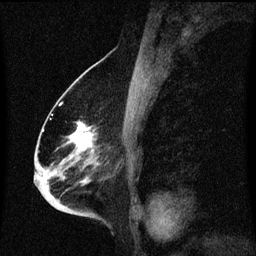
Breast MRI (dynamic contrast-enhanced), one sagittal slice. Slice 37 of 60 in the series (ordered by position). Dynamic contrast-enhanced series, image 2 of 3 at this slice position (ordered by acquisition). 1.5 T. TE 4.2 ms, TR 8.4 ms. 2 mm slice thickness. 256 × 256 image matrix. Patient: female, 68 years. Case-level facts recorded for this patient, not image findings: setting: breast cancer imaged before/during neoadjuvant chemotherapy; receptor status: triple-negative.
Outlined on this slice (semi-automatically segmented with operator editing):
- analysis volume of interest (the breast-tissue region the enhancement analysis was run in; not a lesion): bounding box (x1, y1, x2, y2) in pixels: (37, 96, 113, 213)
- tumour enhancement mask (voxels above the 70 % enhancement threshold inside the analysis volume of interest): (69, 124, 94, 183)